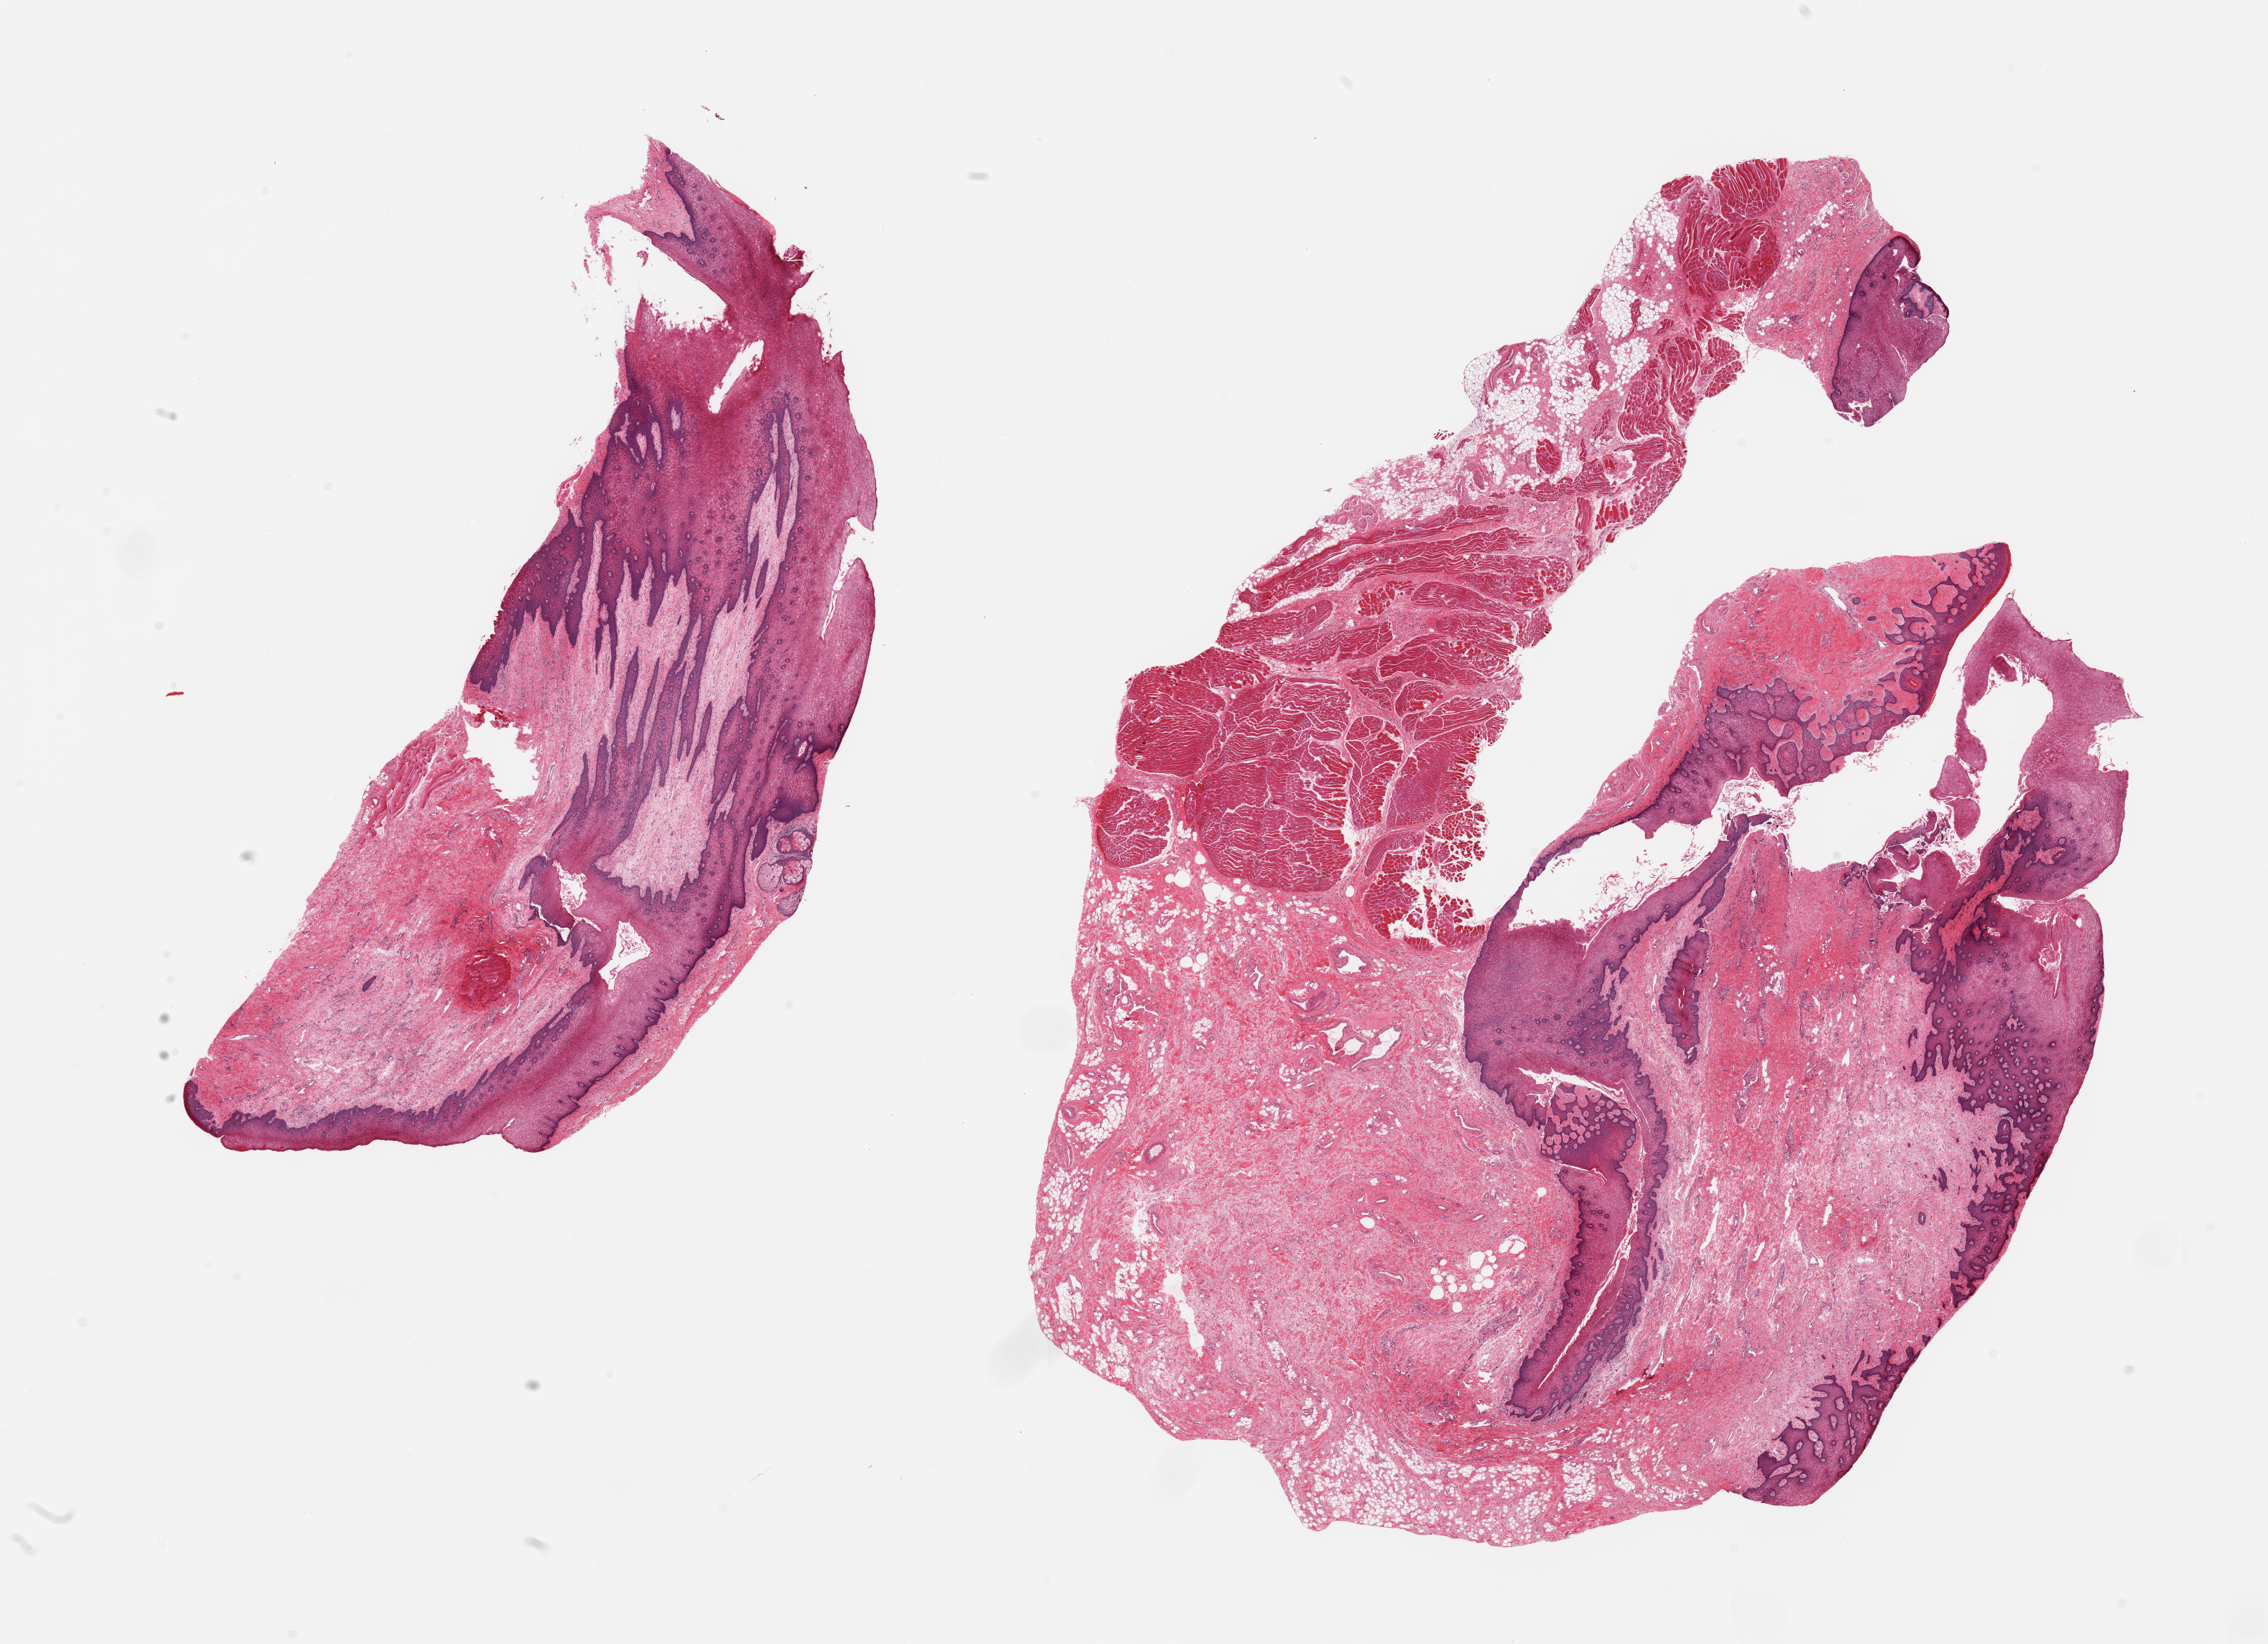
Digitized H&E-stained section, a low-resolution overview of the entire scanned area, about 25.6 x 18.6 mm (acquisition: 20x scan); PAXgene-fixed, paraffin-embedded tissue; sampled site (target tissue): minor salivary gland; tissue donor sample. Donor sex: male.
Review note (as recorded): 2 pieces; lip and skeletal muscle, no glands.